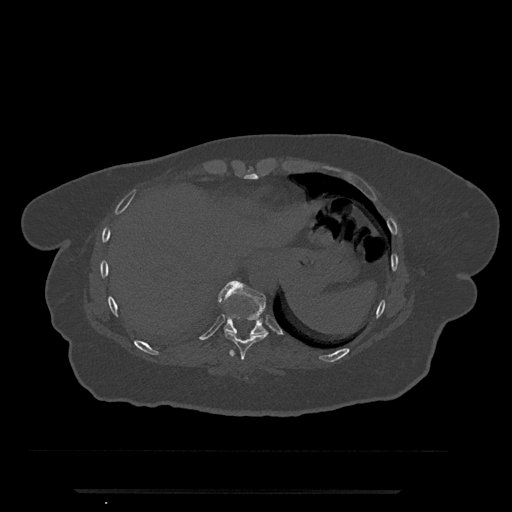
CT including the spine, one axial slice; slice 317 of 797 in the series (ordered by position); reconstruction kernel Br40s/3; bone window (W 1800 / L 400 HU); 0.5 mm slice thickness; 512 × 512 image matrix, field of view 440 × 440 mm. Female patient, age 51 years. From the clinical record (not read from this slice): primary cancer: neuro; vertebrae with lytic lesions (as recorded): T8.
Structures marked on this image (semi-automatically segmented with operator editing):
- T10 vertebra: bounding box [x1, y1, x2, y2] px = [218, 281, 267, 336]
- T9 vertebra: [224, 330, 268, 360]